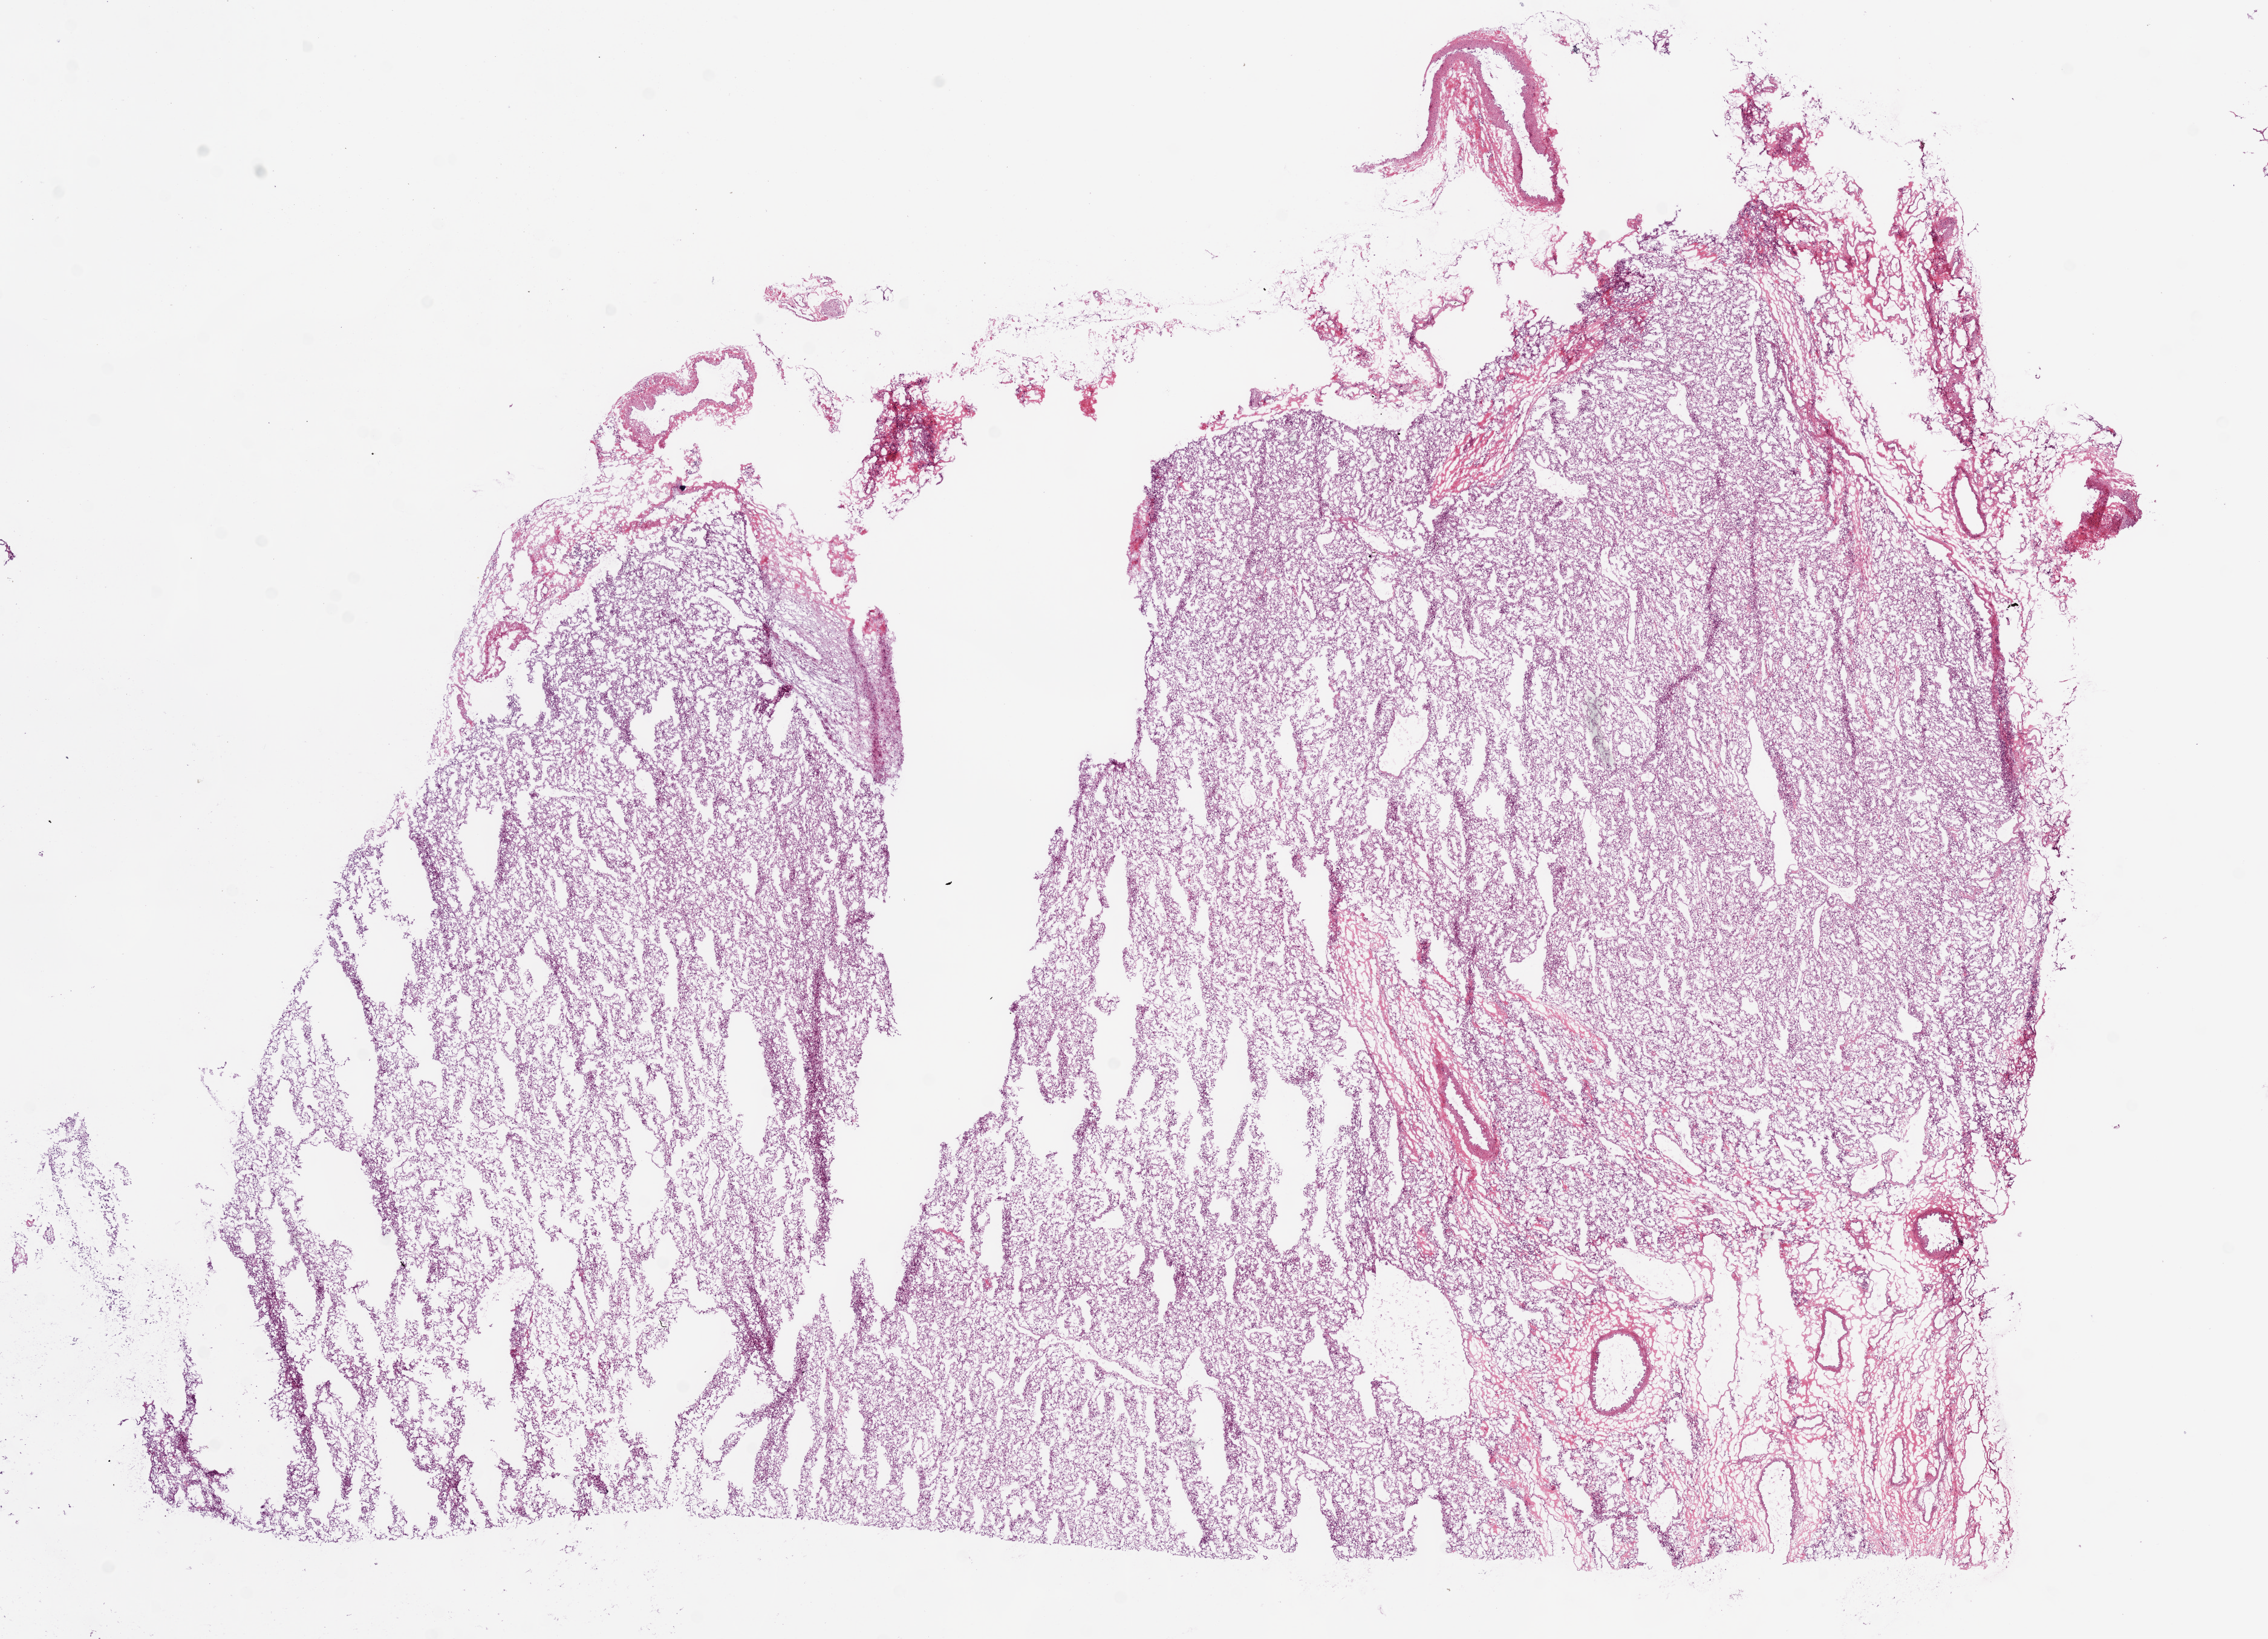
Digitized Hematoxylin and eosin (H&E) stained tissue section (whole slide) — low-resolution overview of the scanned area, about 15.0 x 10.9 mm (from a 20x scan); frozen section; primary tumour sample from the kidney. Male patient; age at initial diagnosis 63 years. Histologic grade: G4 (undifferentiated). Slide review estimates, as recorded: tumour cells 90%, tumour nuclei 85%, normal cells 0%, stromal cells 10%, necrosis 0%.
• AJCC pathologic stage: III
• lymph nodes positive (case pathology): 0 of 15 examined
• diagnosis: Clear cell adenocarcinoma, NOS